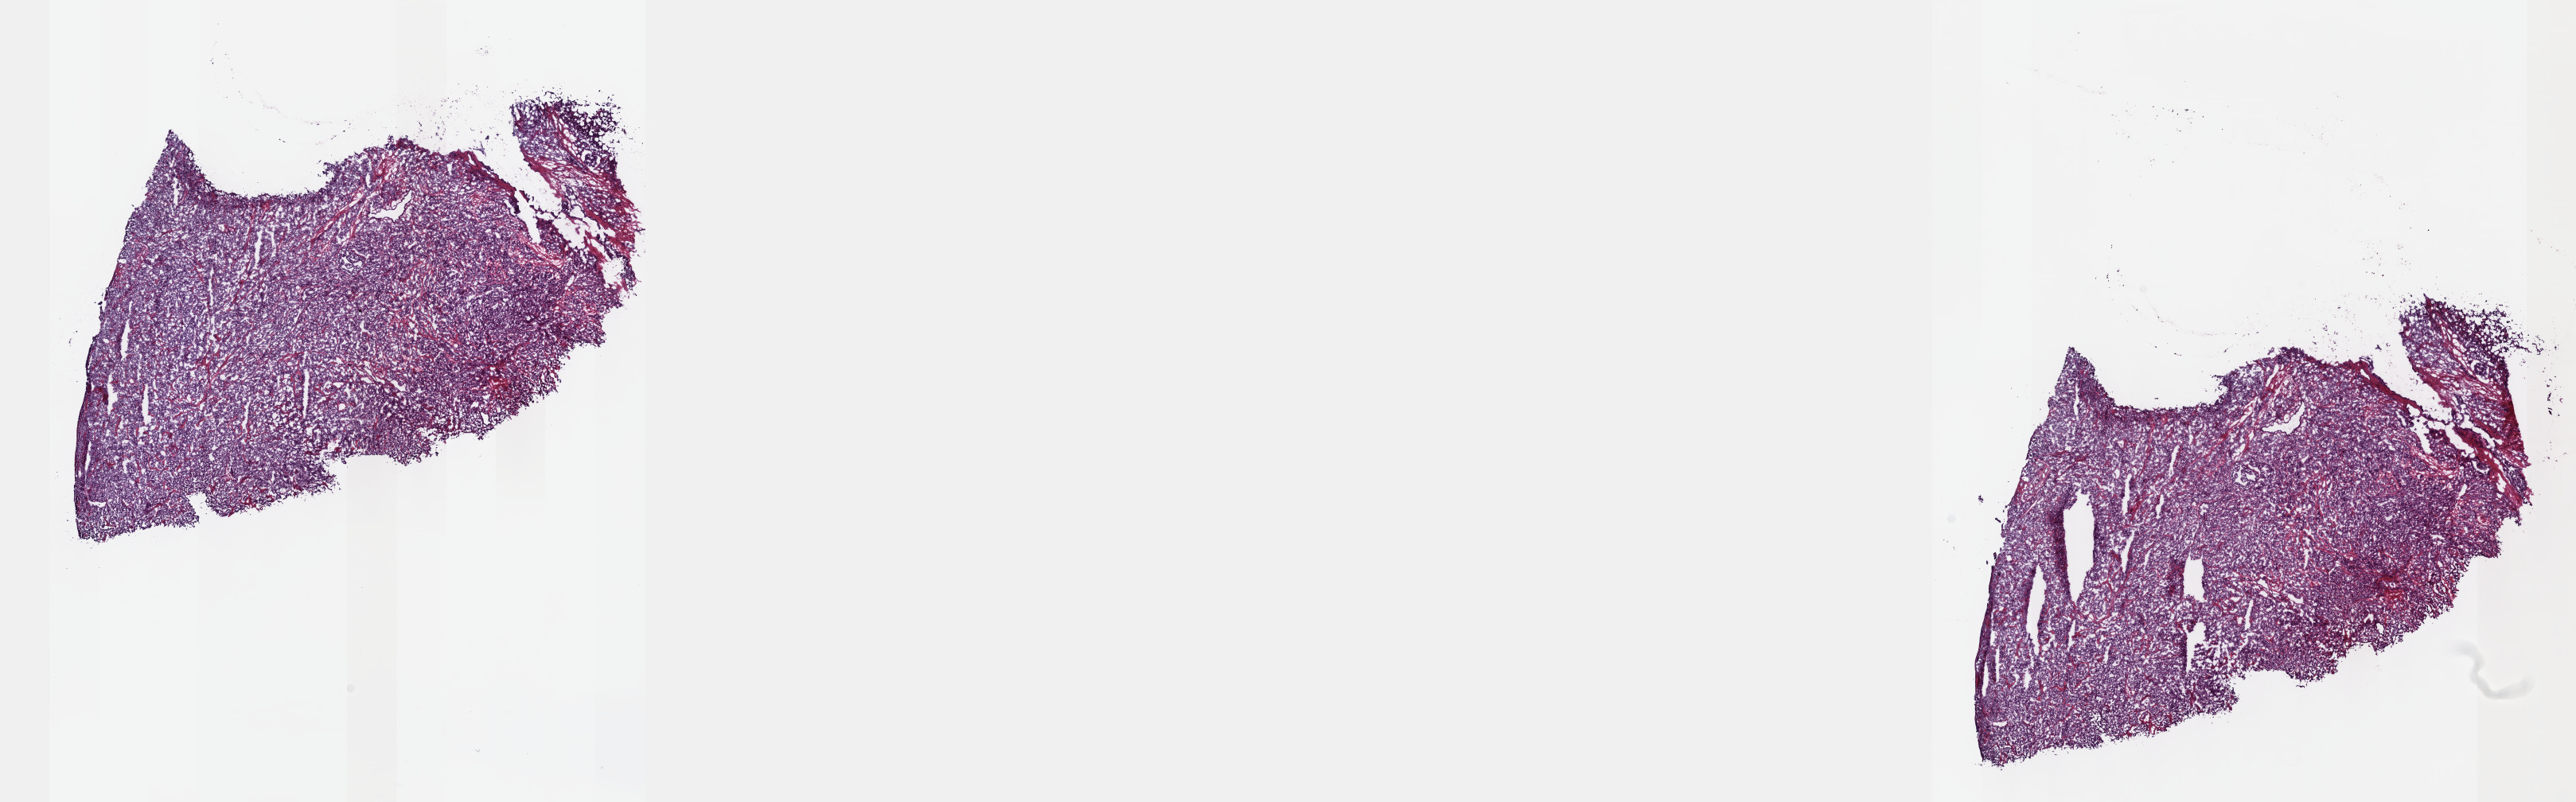
Whole-slide histology image, H&E, low-resolution overview of the scanned area, about 26.2 x 8.1 mm (slide scanned at 40x). Frozen section from the top of the tissue portion. Prostate, primary tumour sample. Male patient; age at initial diagnosis 55 years. Gleason score: 9 (5+4). Pathologist review of this section (percent, as recorded): tumour cells 85%, tumour nuclei 85%, normal cells 0%, stromal cells 15%, necrosis 0%. Infiltration values recorded for this section: lymphocyte infiltration 3%, monocyte infiltration 1%, neutrophil infiltration 1%.
• laterality: bilateral
• pathologic diagnosis: Adenocarcinoma, NOS (prostate gland)